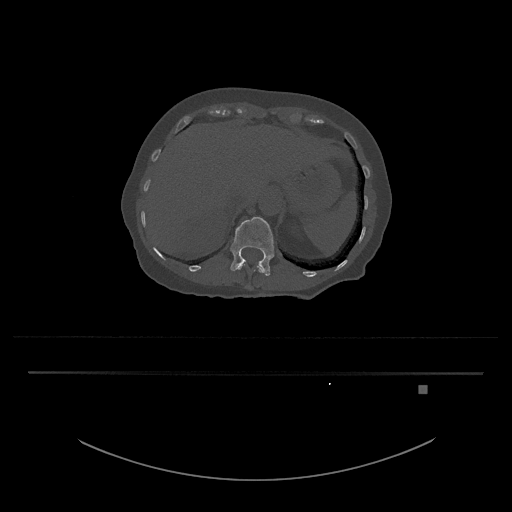
CT including the spine, one axial slice; position 574 of 797 along the scan axis; reconstruction kernel Br40s/3; 120 kVp; bone window (W 1800 / L 400 HU); 0.5 mm slice thickness; 512 × 512 image matrix, field of view 500 × 500 mm. Patient: female, 57 years. Case-level facts recorded for this patient, not image findings: primary cancer: cervical.
Outlined on this slice (semi-automatic segmentation, software-assisted and operator-edited):
- L1 vertebra: box from (x=230, y=217) to (x=274, y=276) px
- T12 vertebra: (x=236, y=262)–(x=264, y=273)